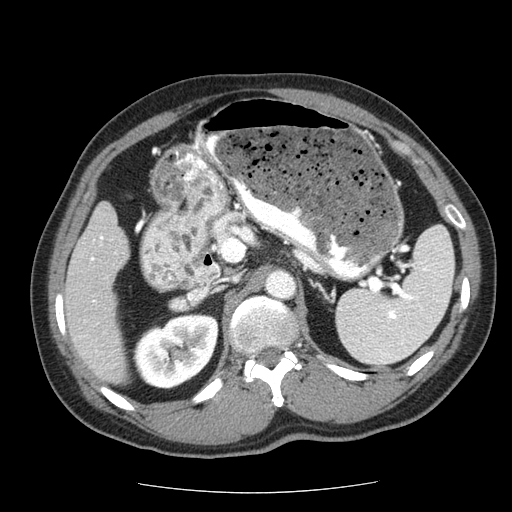
Contrast-enhanced abdominal CT (liver protocol), one axial slice; slice 24 of 85 in the series (ordered by position); 120 kVp; soft-tissue window (W 400 / L 40 HU); 2.5 mm slice thickness; 512 × 512 image matrix, field of view 360 × 360 mm. From the clinical record (not read from this slice): diagnosis: hepatocellular carcinoma (patient treated with transarterial chemoembolisation; whether this scan precedes or follows treatment is not stated here); TNM stage (as recorded): Stage-IIIA; Child-Pugh class: A; tumour differentiation: well differentiated; tumour nodularity: multinodular.
Structures marked on this image (semi-automatic segmentation, software-assisted and operator-edited):
- liver parenchyma outside the tumour (the mass and vessels are separate outlines, so this box may not span the whole liver): bounding box [x1, y1, x2, y2] px = [64, 202, 128, 384]
- liver vessels: [90, 236, 104, 302]